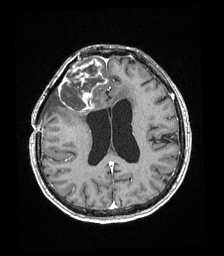
Brain MRI from a brain-tumour surgery series, one axial slice. Position 82 of 192 along the scan axis. T1-weighted post-contrast. 1 mm slice thickness. 224 × 256 image matrix, field of view 219 × 250 mm. Case-level facts recorded for this patient, not image findings: histopathology: Astrocytoma; WHO grade: 4; IDH mutation: yes; tumour location: Right superficial frontal.
Structures marked on this image (outlined manually by an expert reader):
- tumour: bounding box (x1, y1, x2, y2) in pixels: (59, 59, 107, 111)